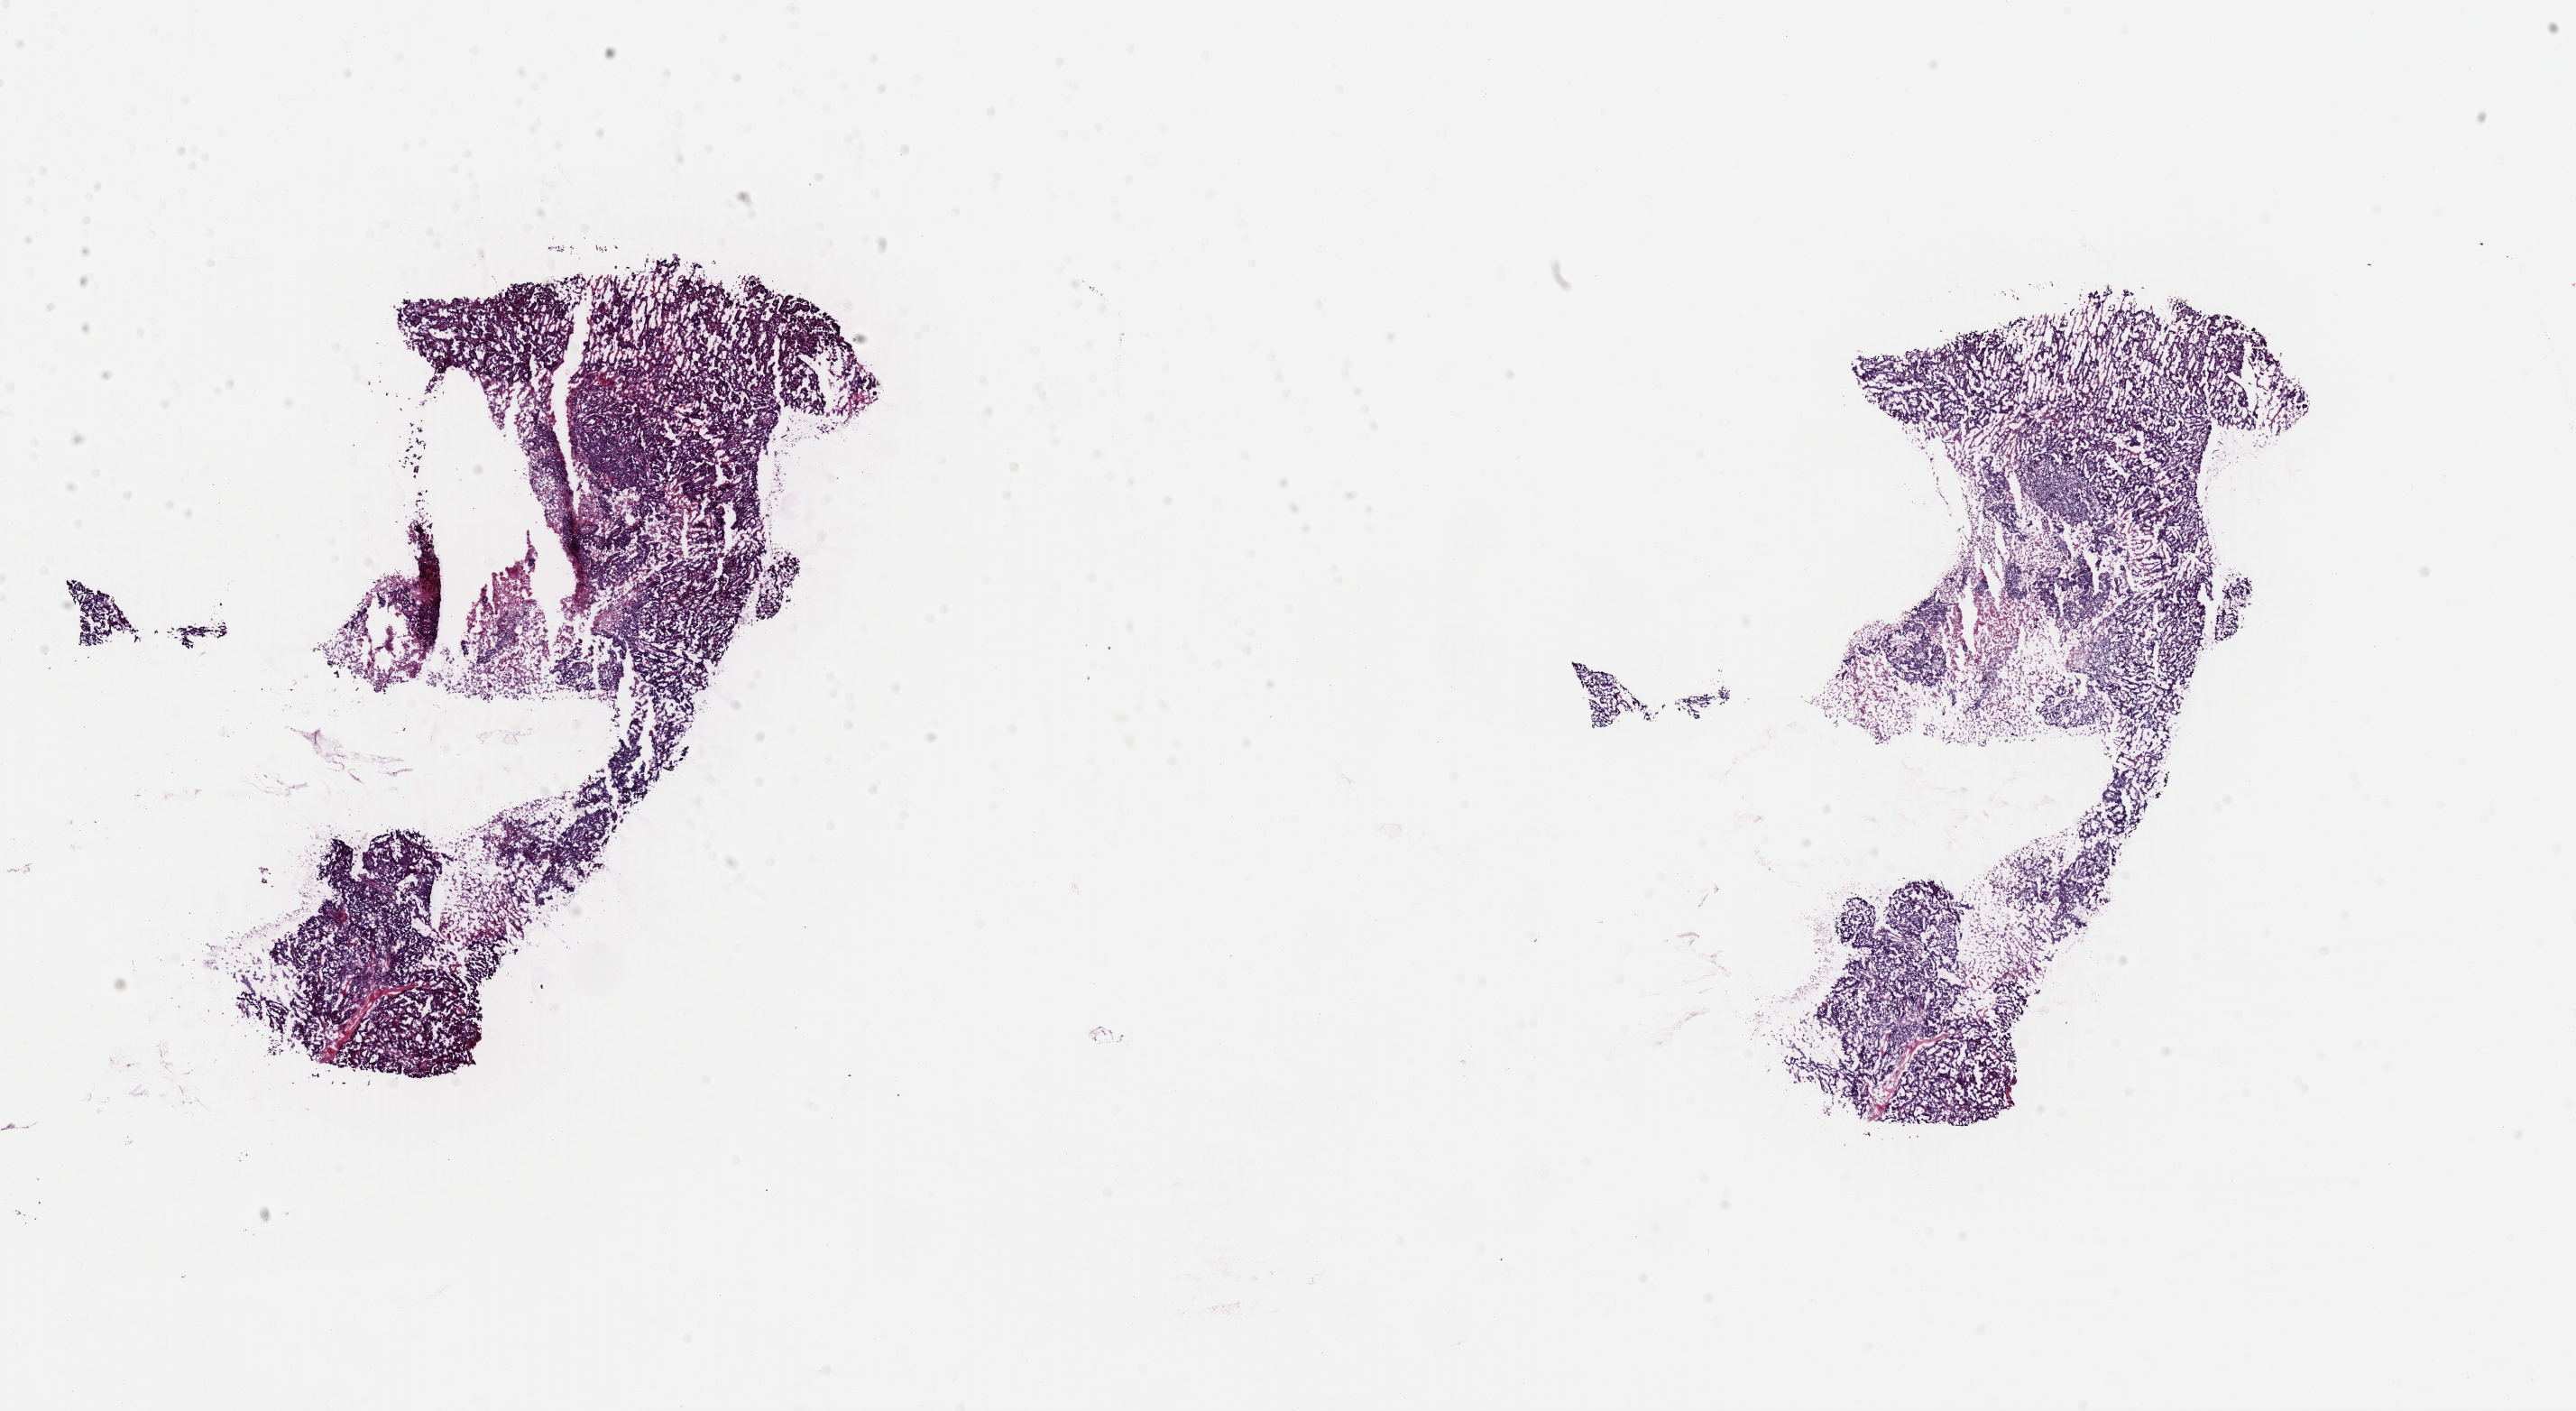
Whole-slide histology image, H&E — a low-resolution overview of the entire scanned area, about 22.6 x 12.4 mm (acquisition: 40x scan), frozen section from the top of the tissue portion, primary tumour sample from the uterus. Patient: female, age at initial diagnosis 58 years. Histologic grade: G3 (poorly differentiated). Composition of this section per pathologist review: tumour cells 82%, tumour nuclei 97%, normal cells 0%, stromal cells 3%, necrosis 15%. Infiltration values recorded for this section: lymphocyte infiltration 0%, monocyte infiltration 0%, neutrophil infiltration 0%.
Lymph nodes positive (case pathology): 0 of 3 examined. FIGO stage: IIIA. Histologic diagnosis: Serous cystadenocarcinoma, NOS (endometrium).